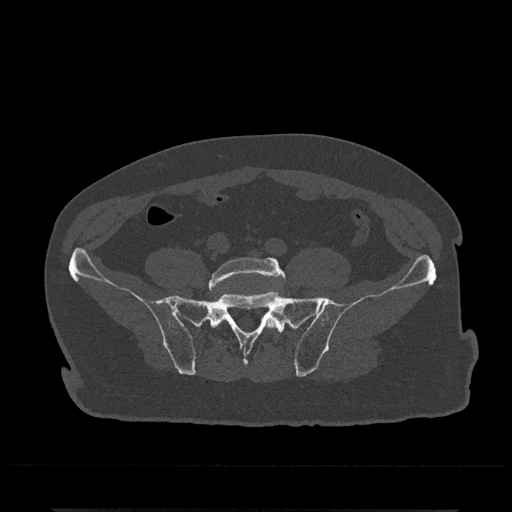
CT including the spine, one axial slice. Slice 46 of 797 in the series (ordered by position). Reconstruction kernel Br40s/3. 120 kVp. Bone window (W 1800 / L 400 HU). 0.5 mm slice thickness. 512 × 512 image matrix, field of view 393 × 393 mm. Male patient, age 67 years. From the clinical record (not read from this slice): primary cancer: prostate.
Structures marked on this image (semi-automatic segmentation, software-assisted and operator-edited):
- L5 vertebra: bounding box [x1, y1, x2, y2] px = [208, 257, 286, 330]